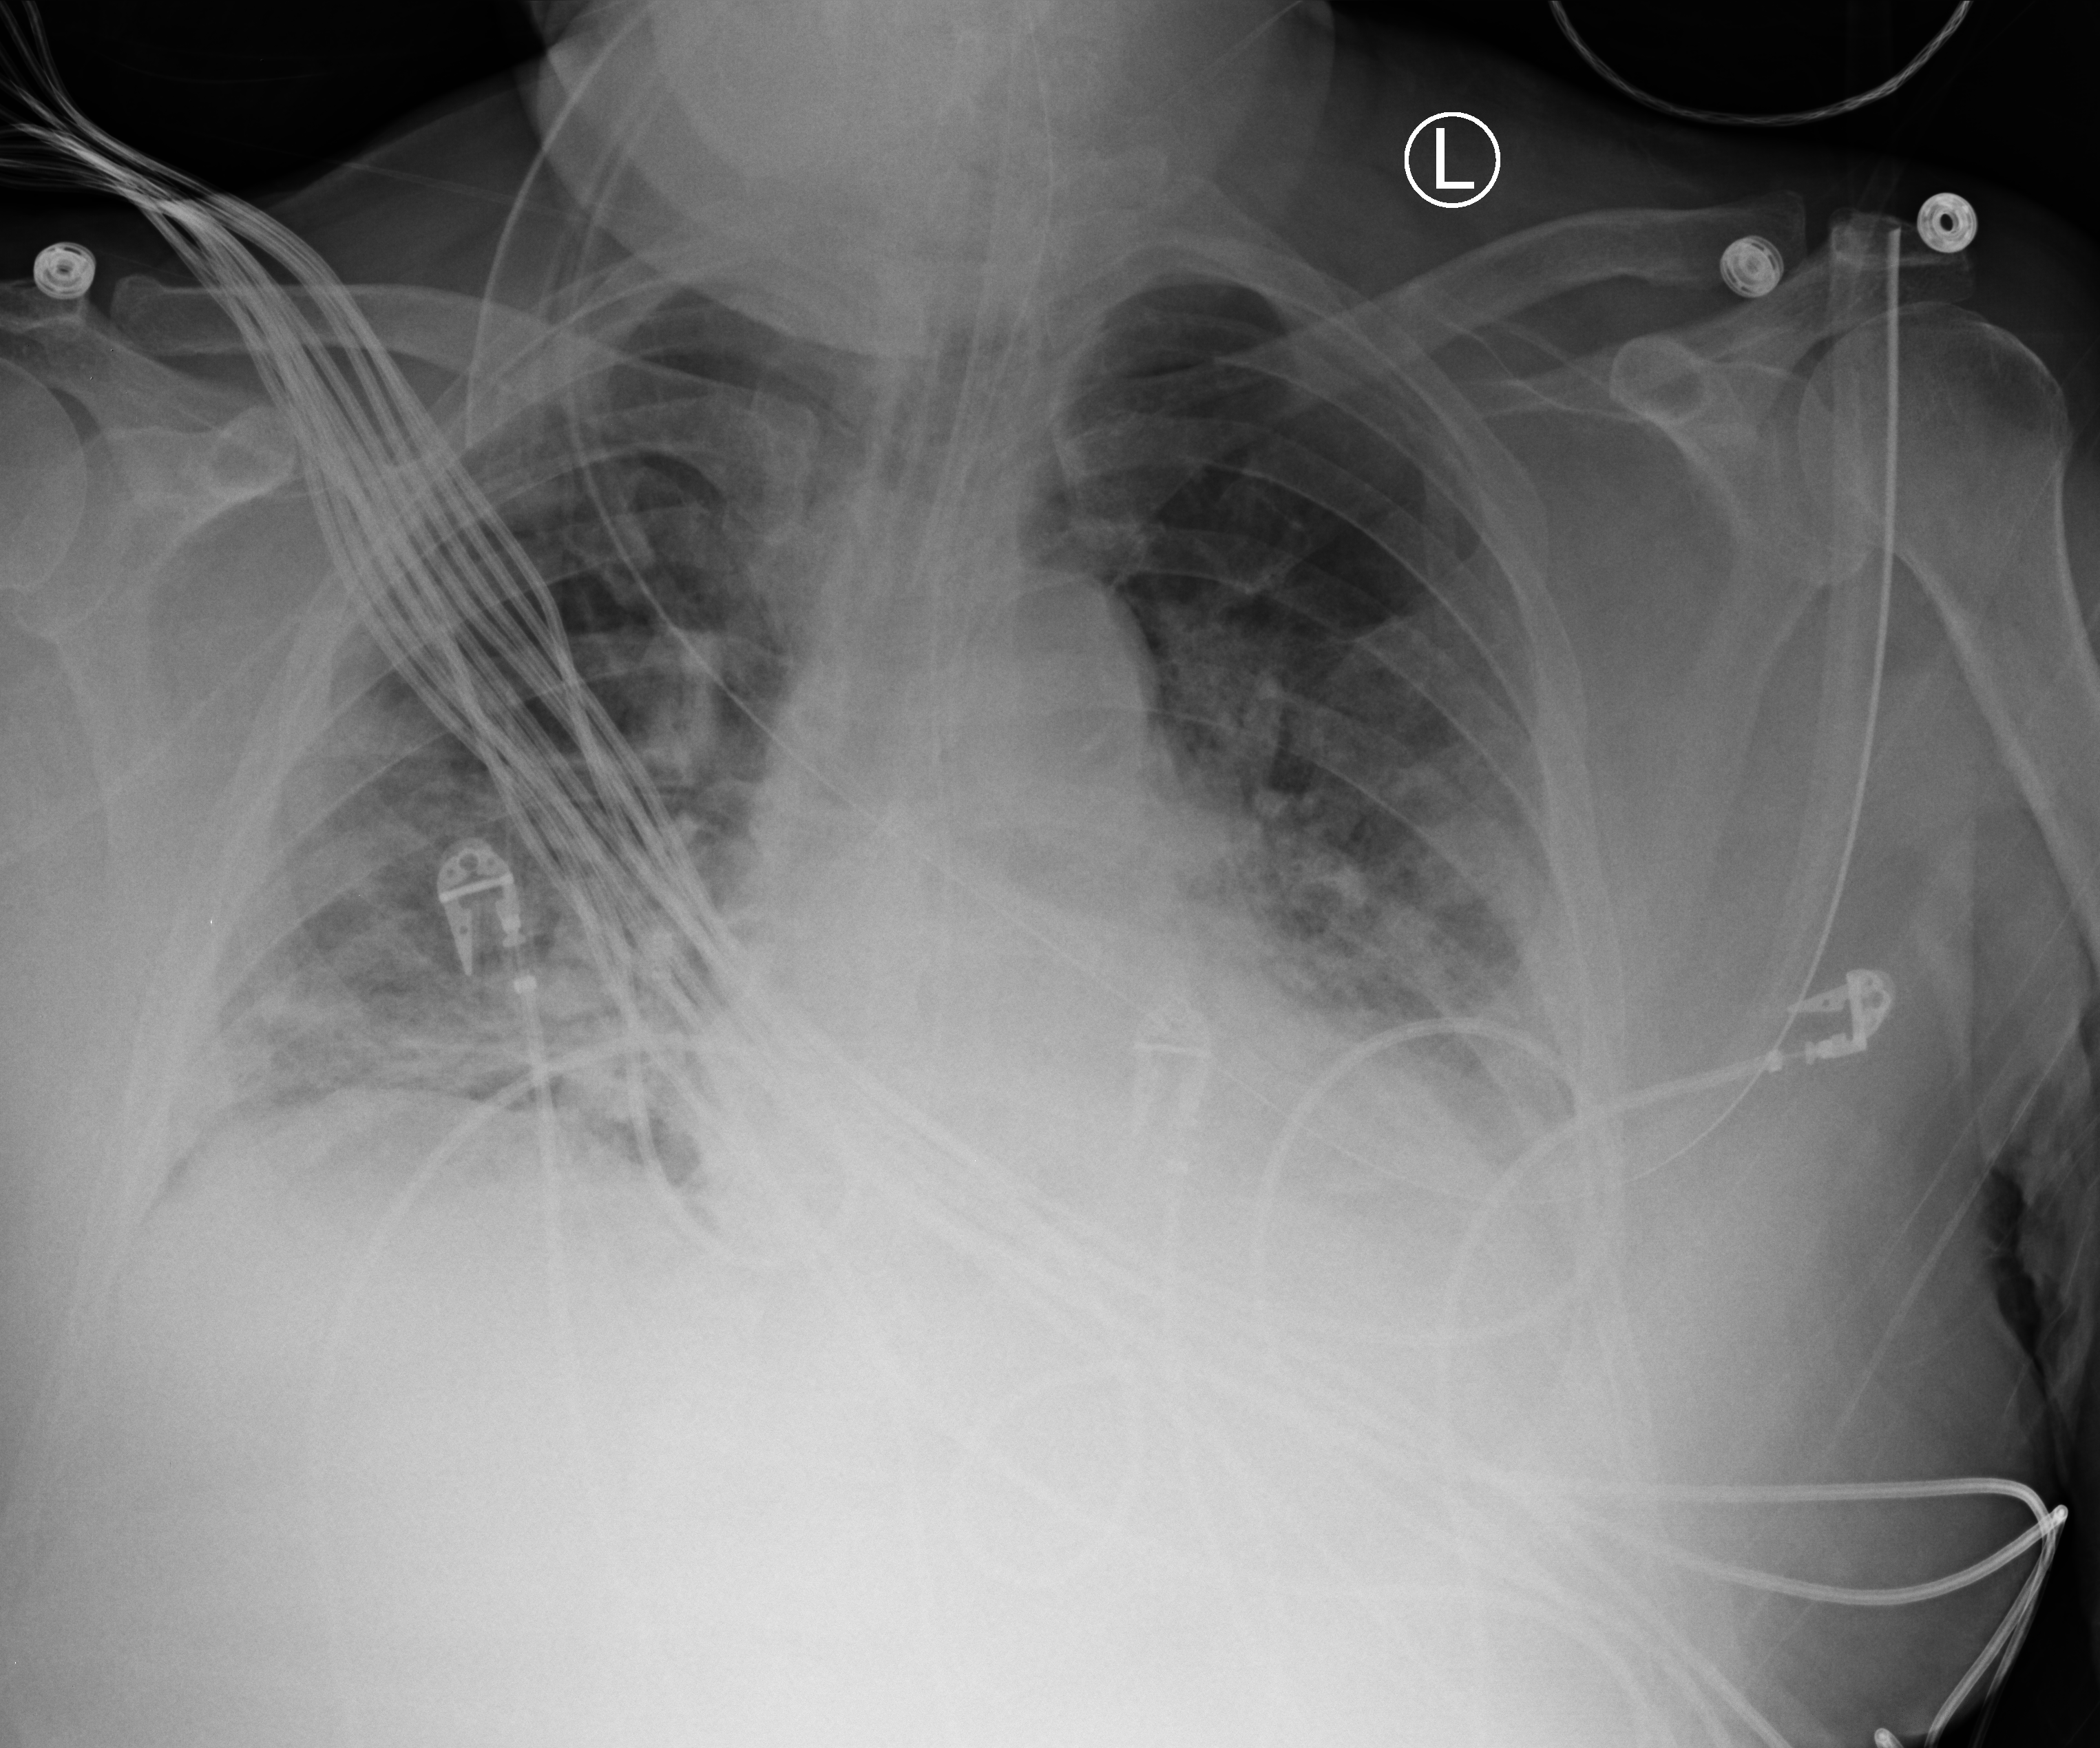
Portable chest radiograph; anteroposterior (AP) projection. Male patient hospitalised with COVID-19, age 60–74 years.
Admission-level facts for this patient (not findings on this image; timing relative to this image not recorded): mechanically ventilated during this hospital stay: yes; hypertension (admission record): yes.